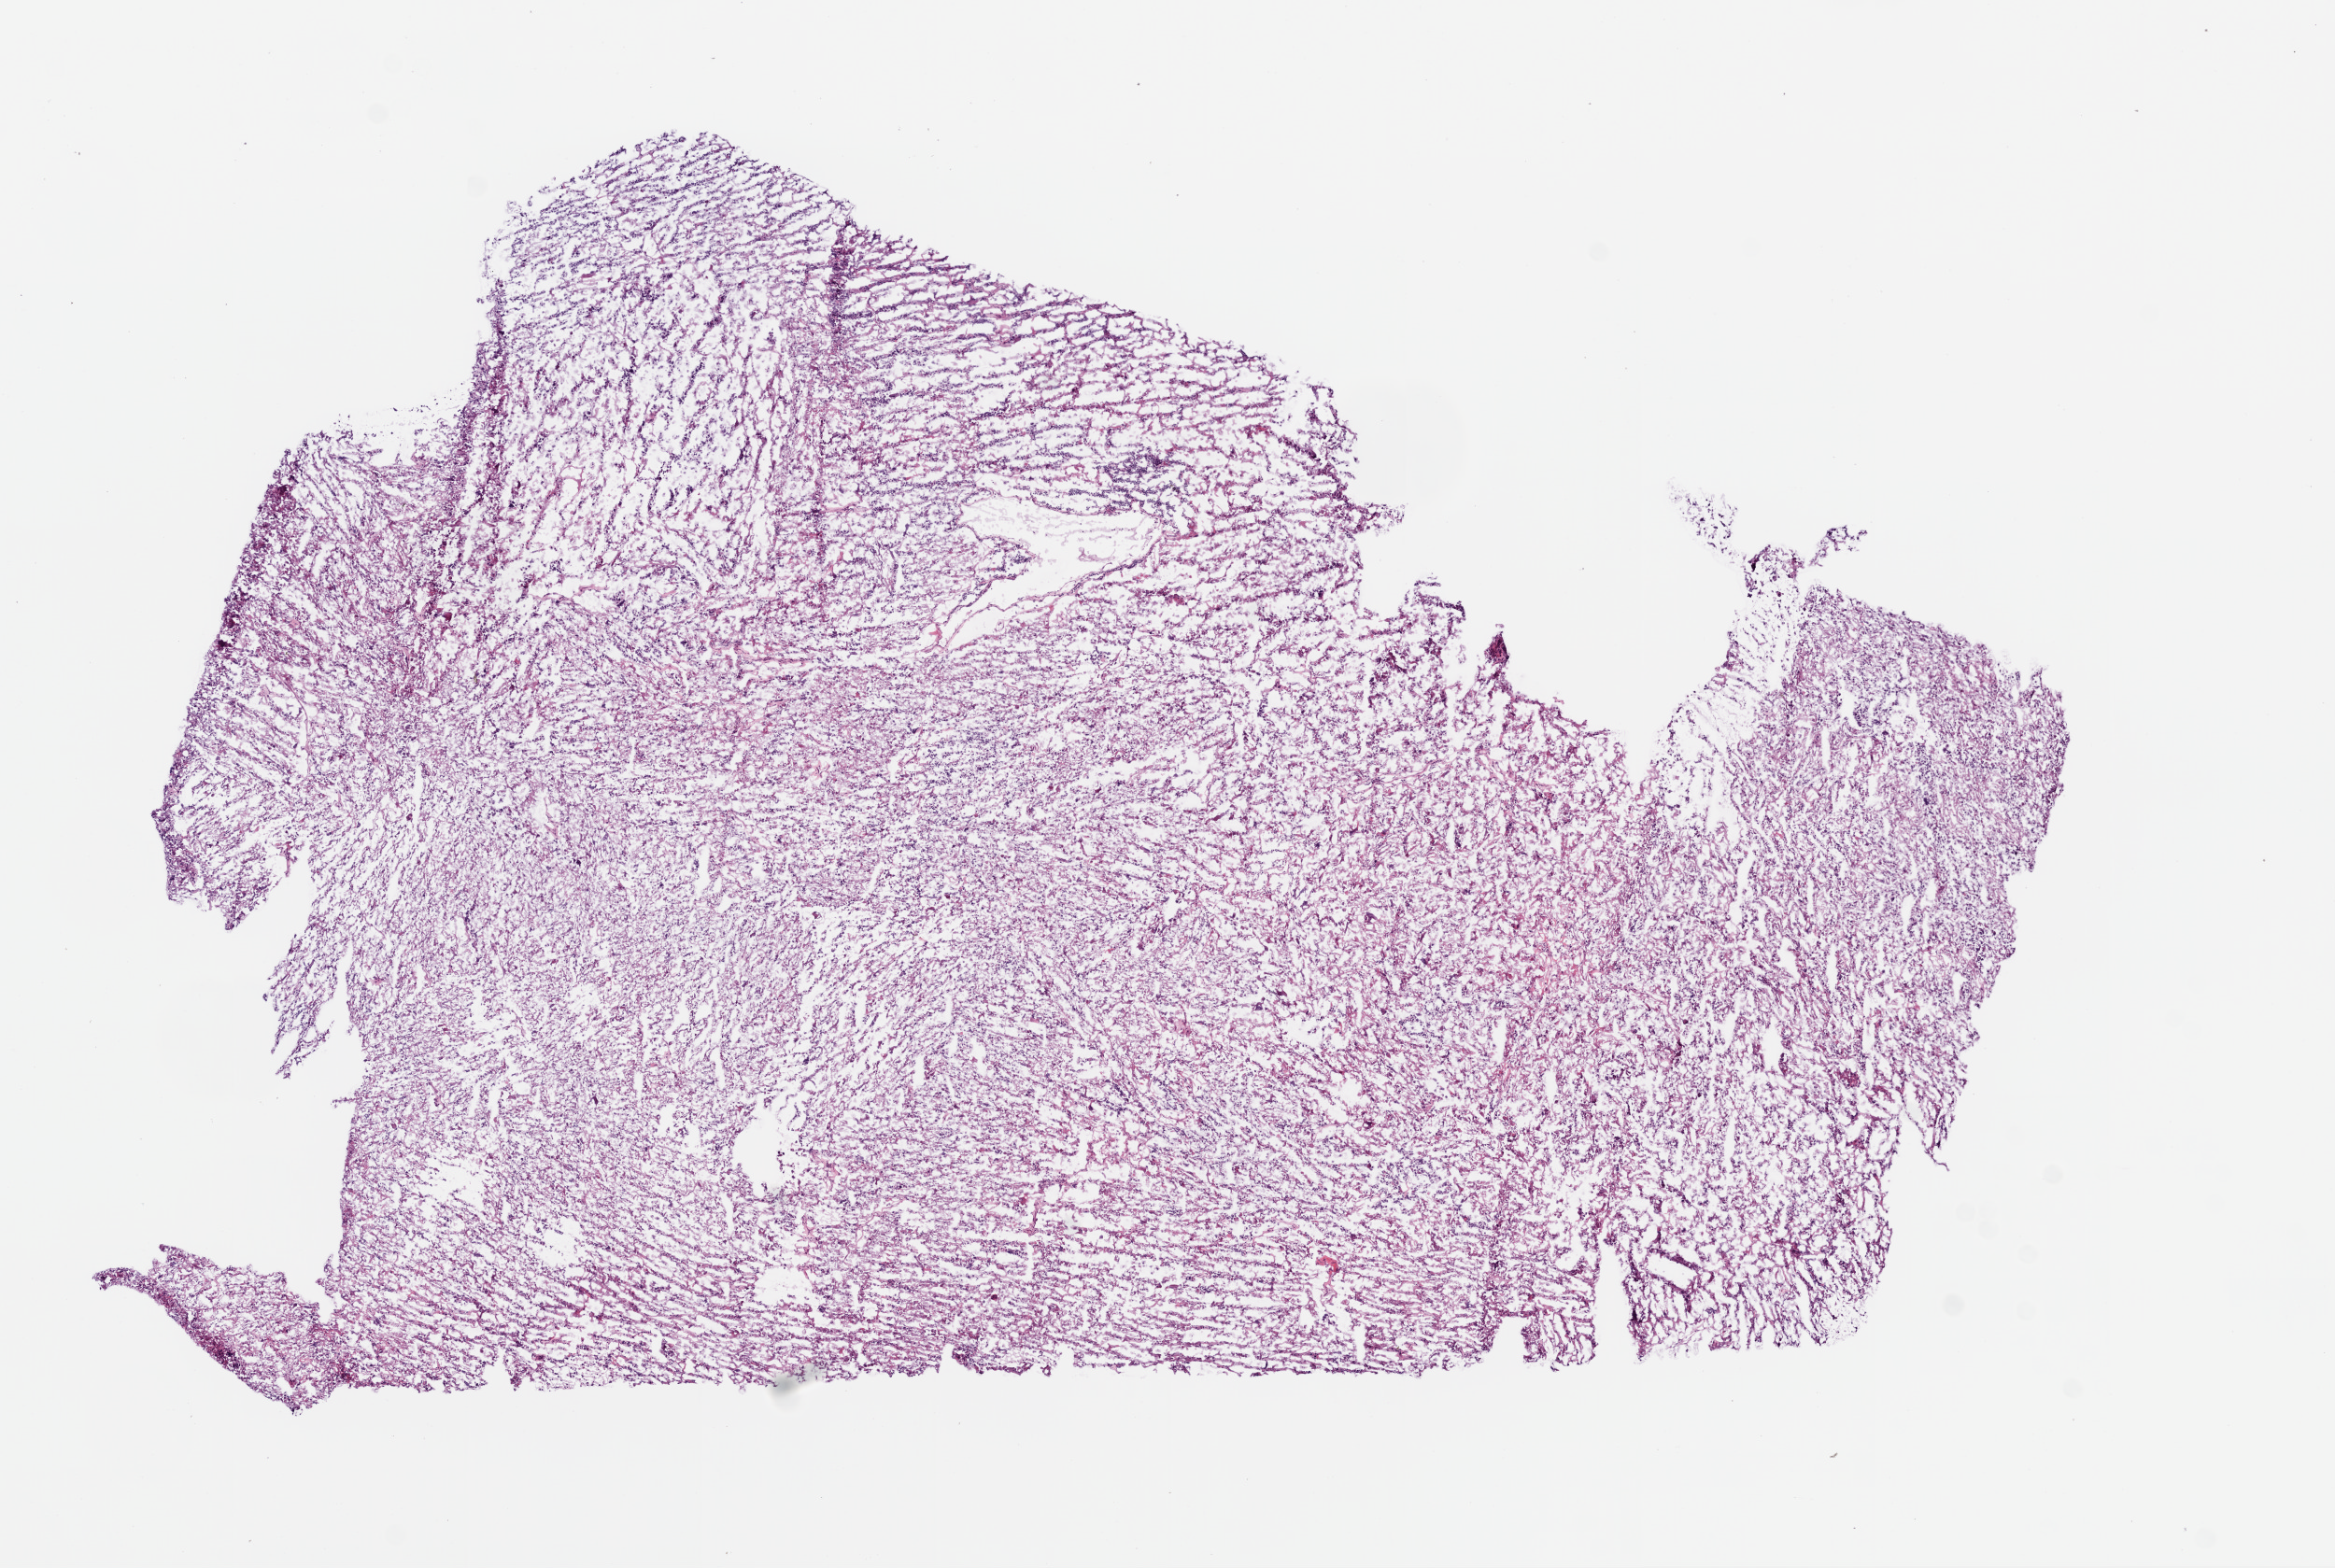
Digitized Hematoxylin and eosin (H&E) stained tissue section (whole slide), whole scanned area (about 10.0 x 6.7 mm, from a 20x scan) shown as a low-resolution overview, frozen section, primary tumour sample from the brain. Patient: male, age at initial diagnosis 59 years. Pathologist review of this section (percent, as recorded): tumour cells 100%, tumour nuclei 75%, normal cells 0%, stromal cells 0%, necrosis 0%.
Diagnosis: Glioblastoma.